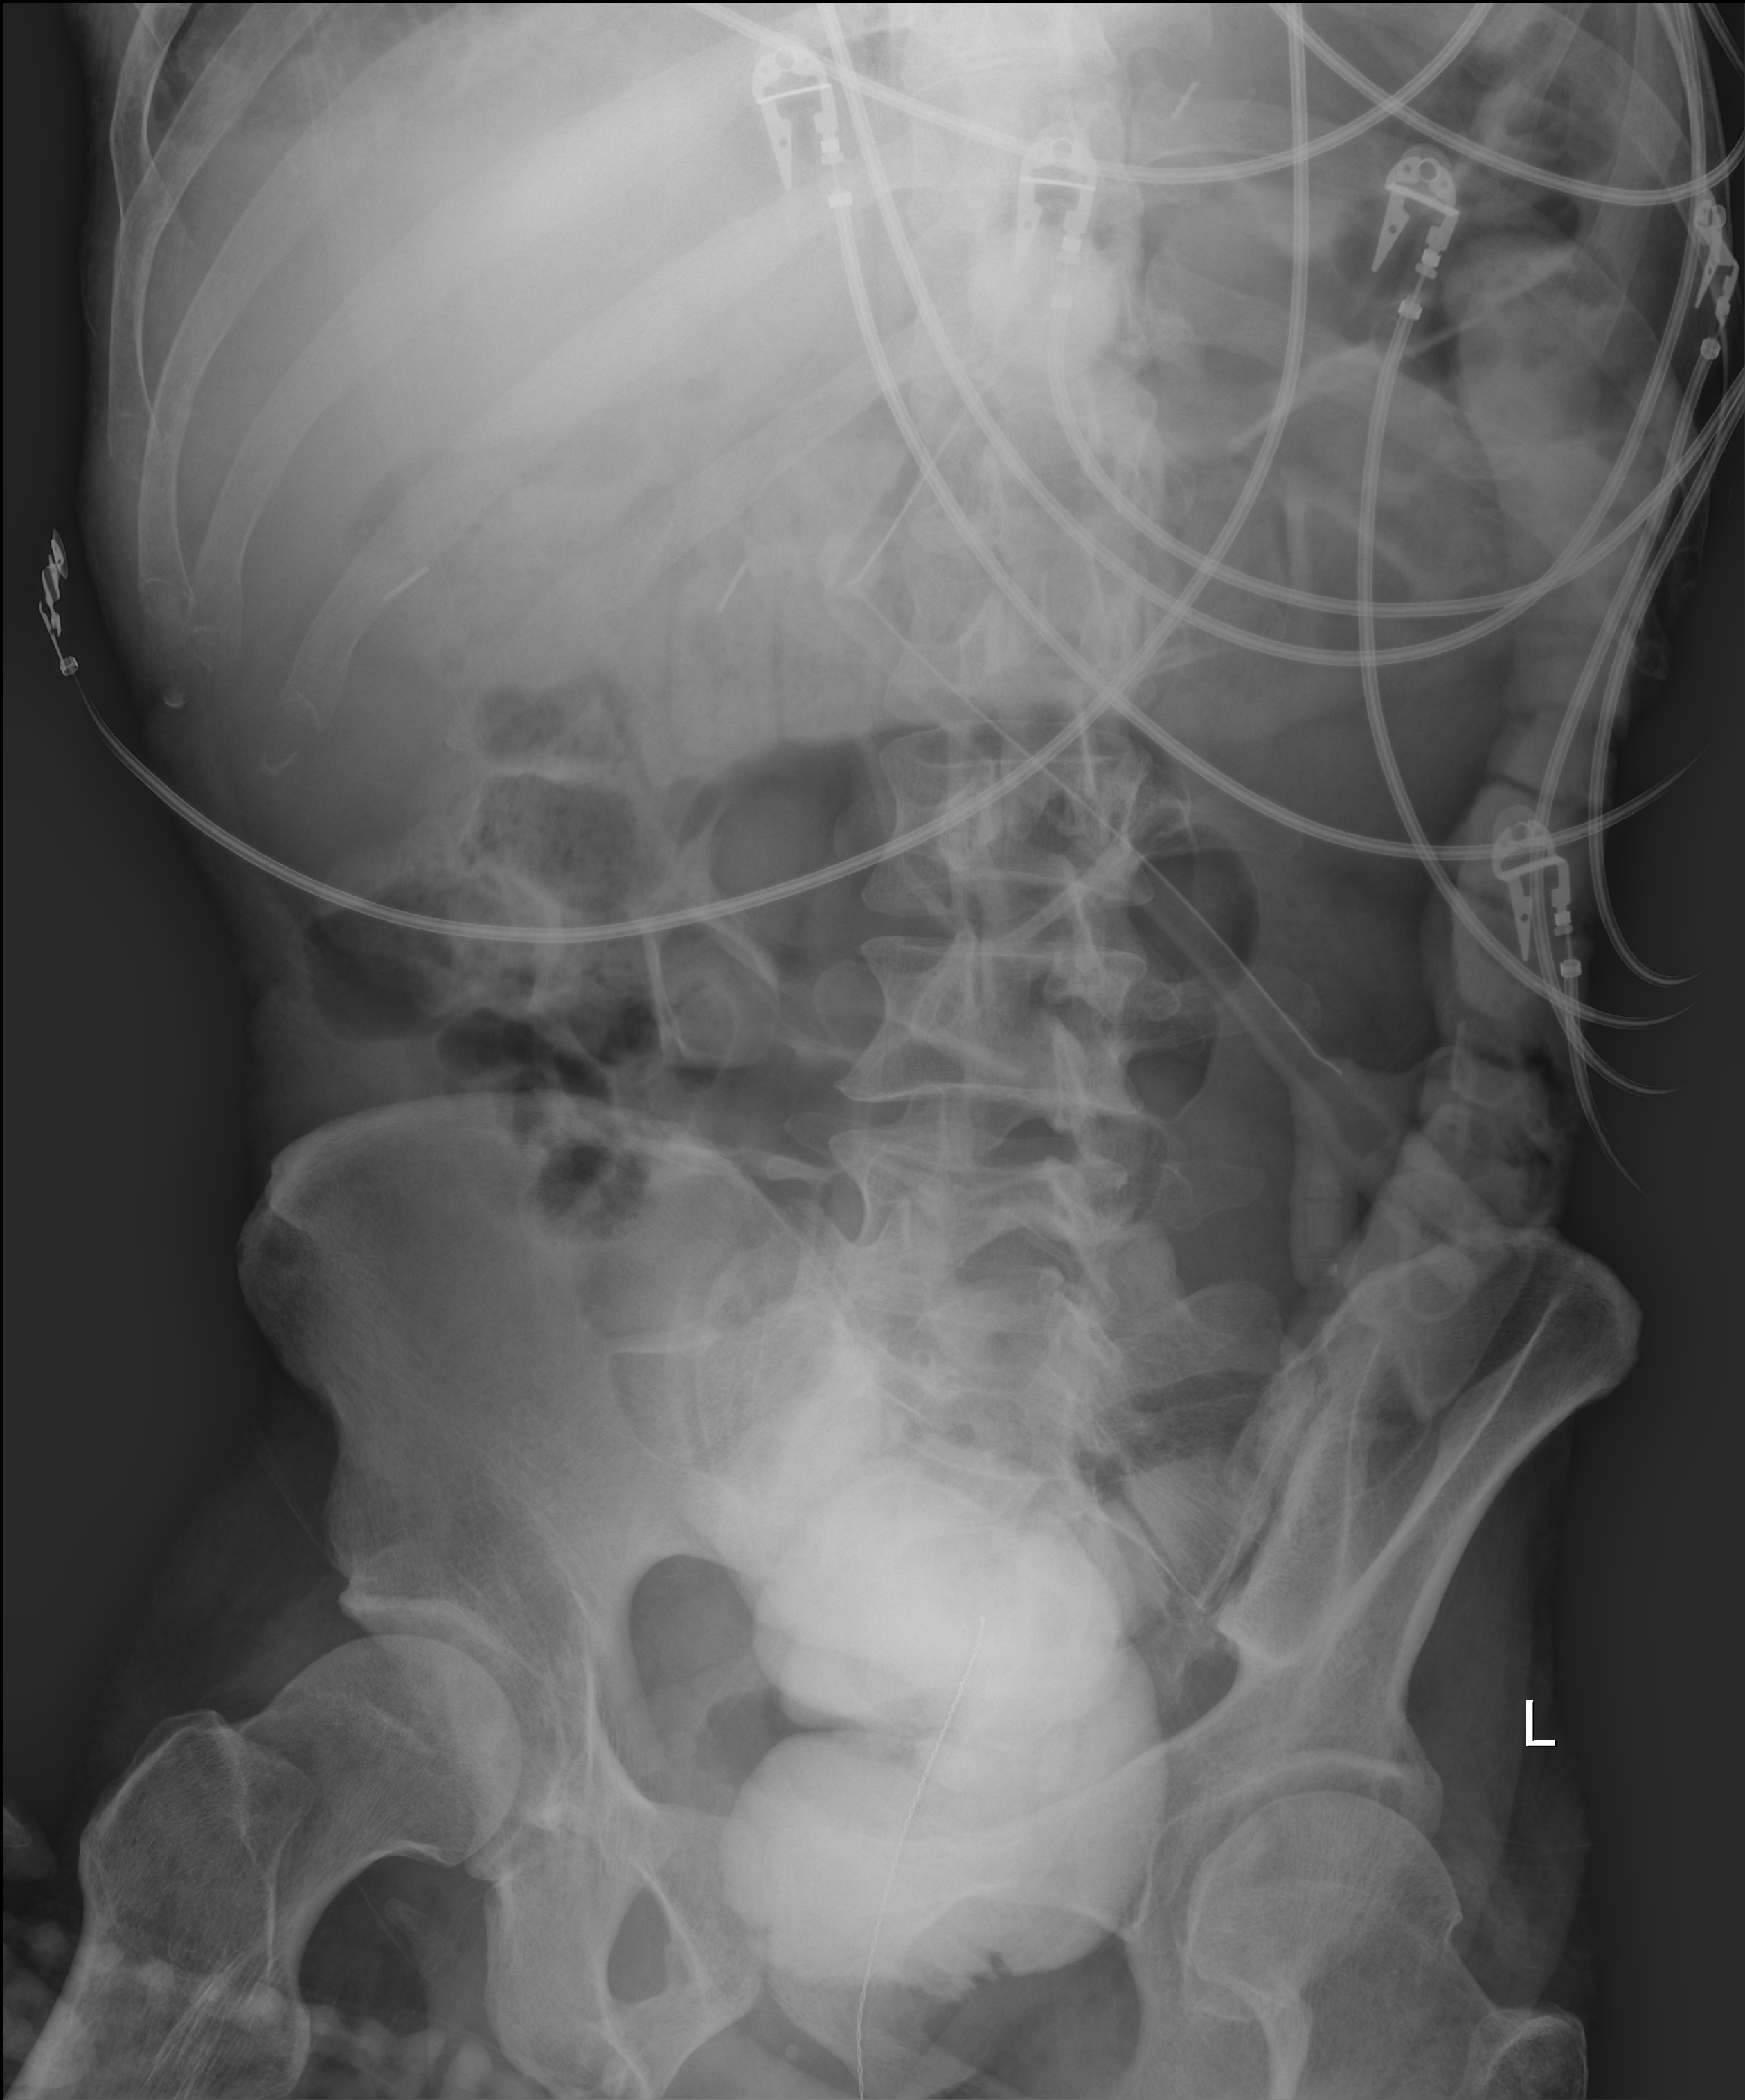
Portable abdomen radiograph; anteroposterior (AP) projection. Patient hospitalised with COVID-19; male, aged 18–59 years.
Admission-level facts for this patient (not findings on this image; timing relative to this image not recorded): mechanically ventilated during this hospital stay: yes; admitted to intensive care during this hospital stay: yes; length of hospital stay: 96 days.